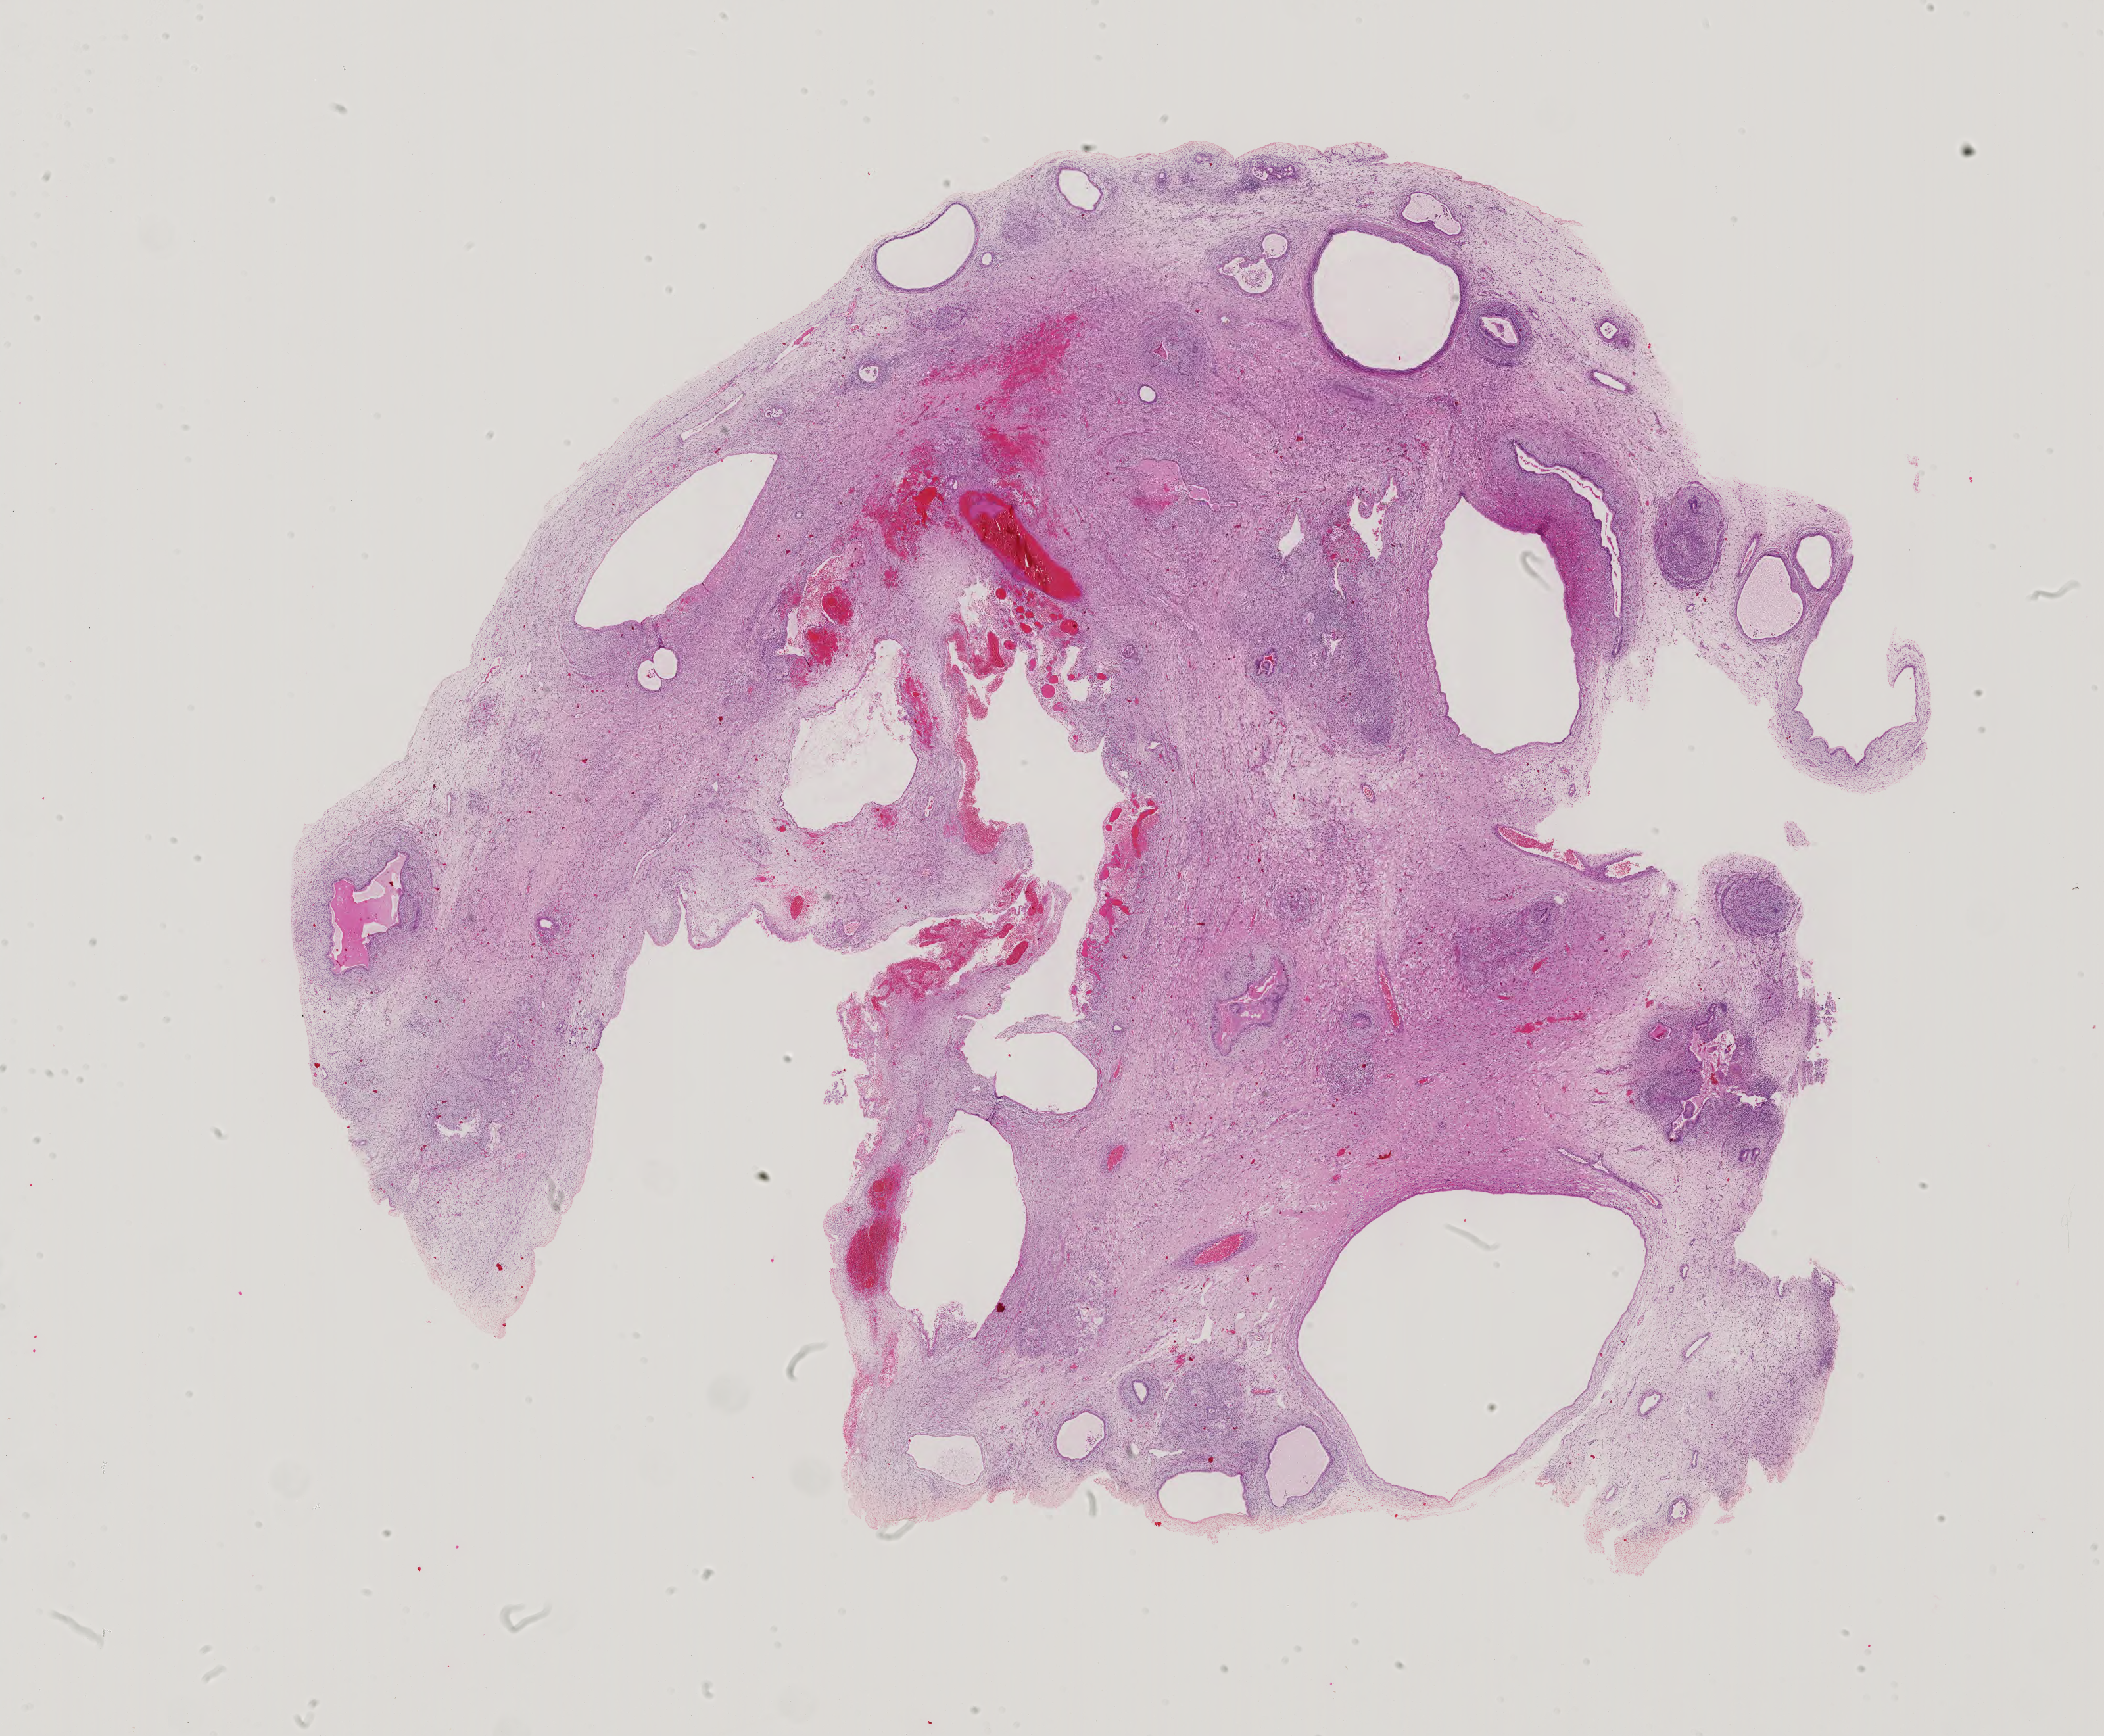
Hematoxylin and eosin (H&E) stained whole-slide image, shown as a low-resolution overview of the whole scanned area (about 23.3 x 19.2 mm). Male patient.
Specimen: formalin-fixed paraffin-embedded (FFPE) diagnostic section; testis, primary tumour sample.